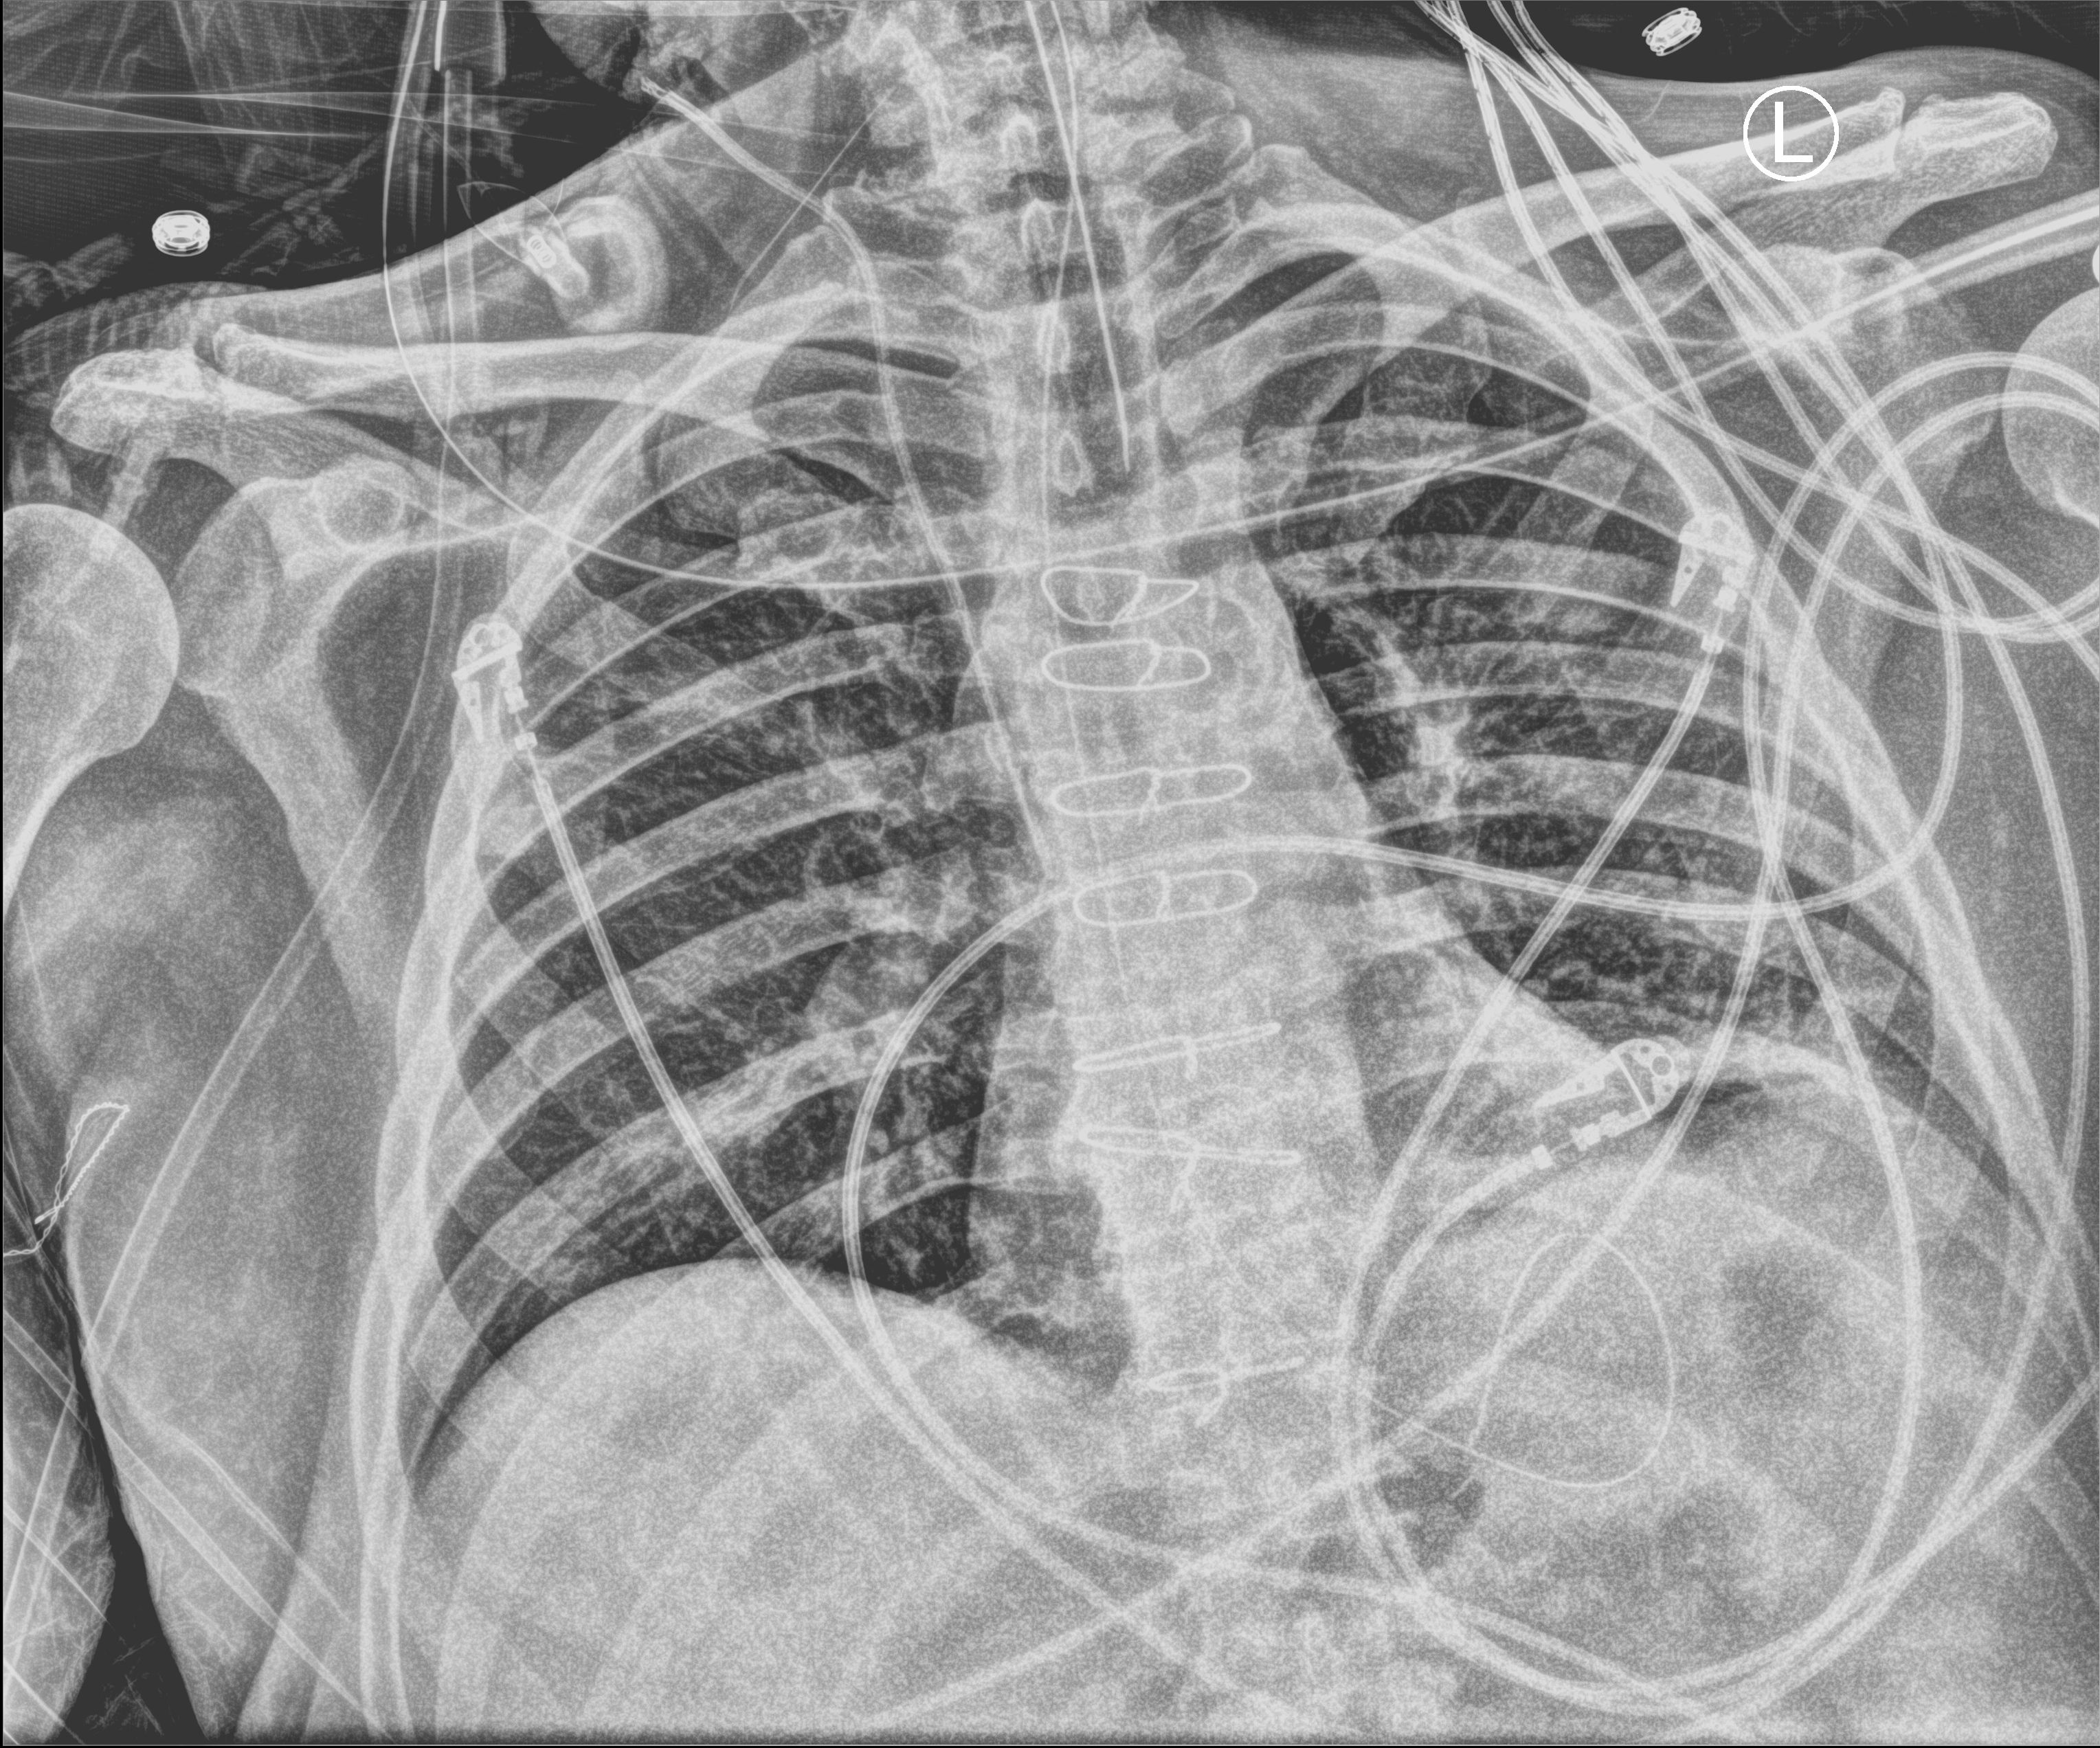
Bedside chest radiograph (computed radiography); anteroposterior (AP) projection. Male patient hospitalised with COVID-19, age 60–74 years.
Hospital-stay facts (about this admission, not read from this image; timing relative to this image not recorded): diabetes (admission record): yes; mechanically ventilated during this hospital stay: yes.